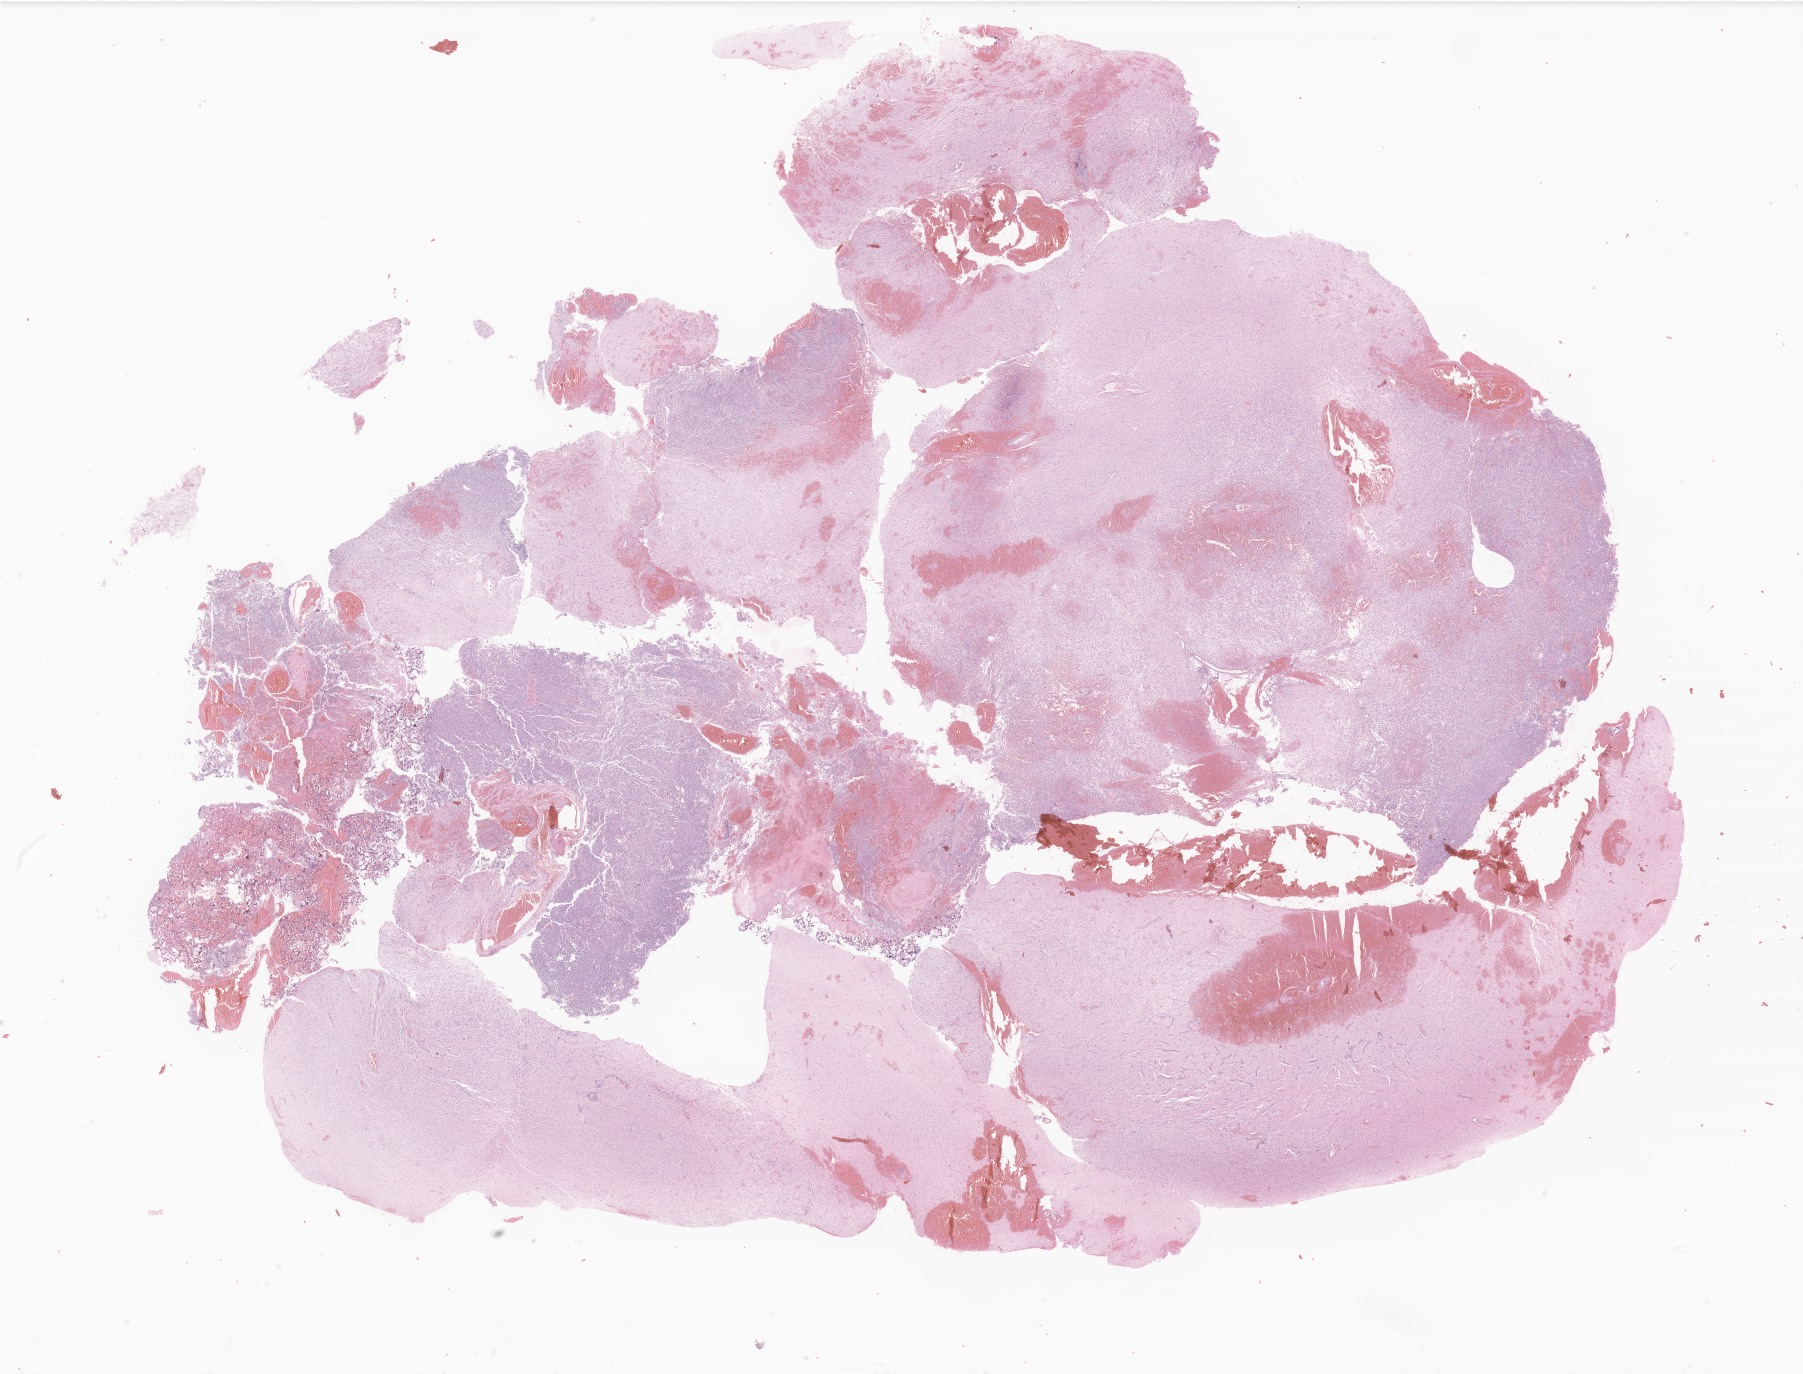
Digitized hematoxylin and eosin (H&E)-stained section of tumor tissue from the brain — low-resolution overview of the scanned area, about 30.4 x 23.2 mm. Formalin-fixed paraffin-embedded section. Patient: male, age 214 months (17 years 10 months).
Diagnosis: Glioma, malignant.